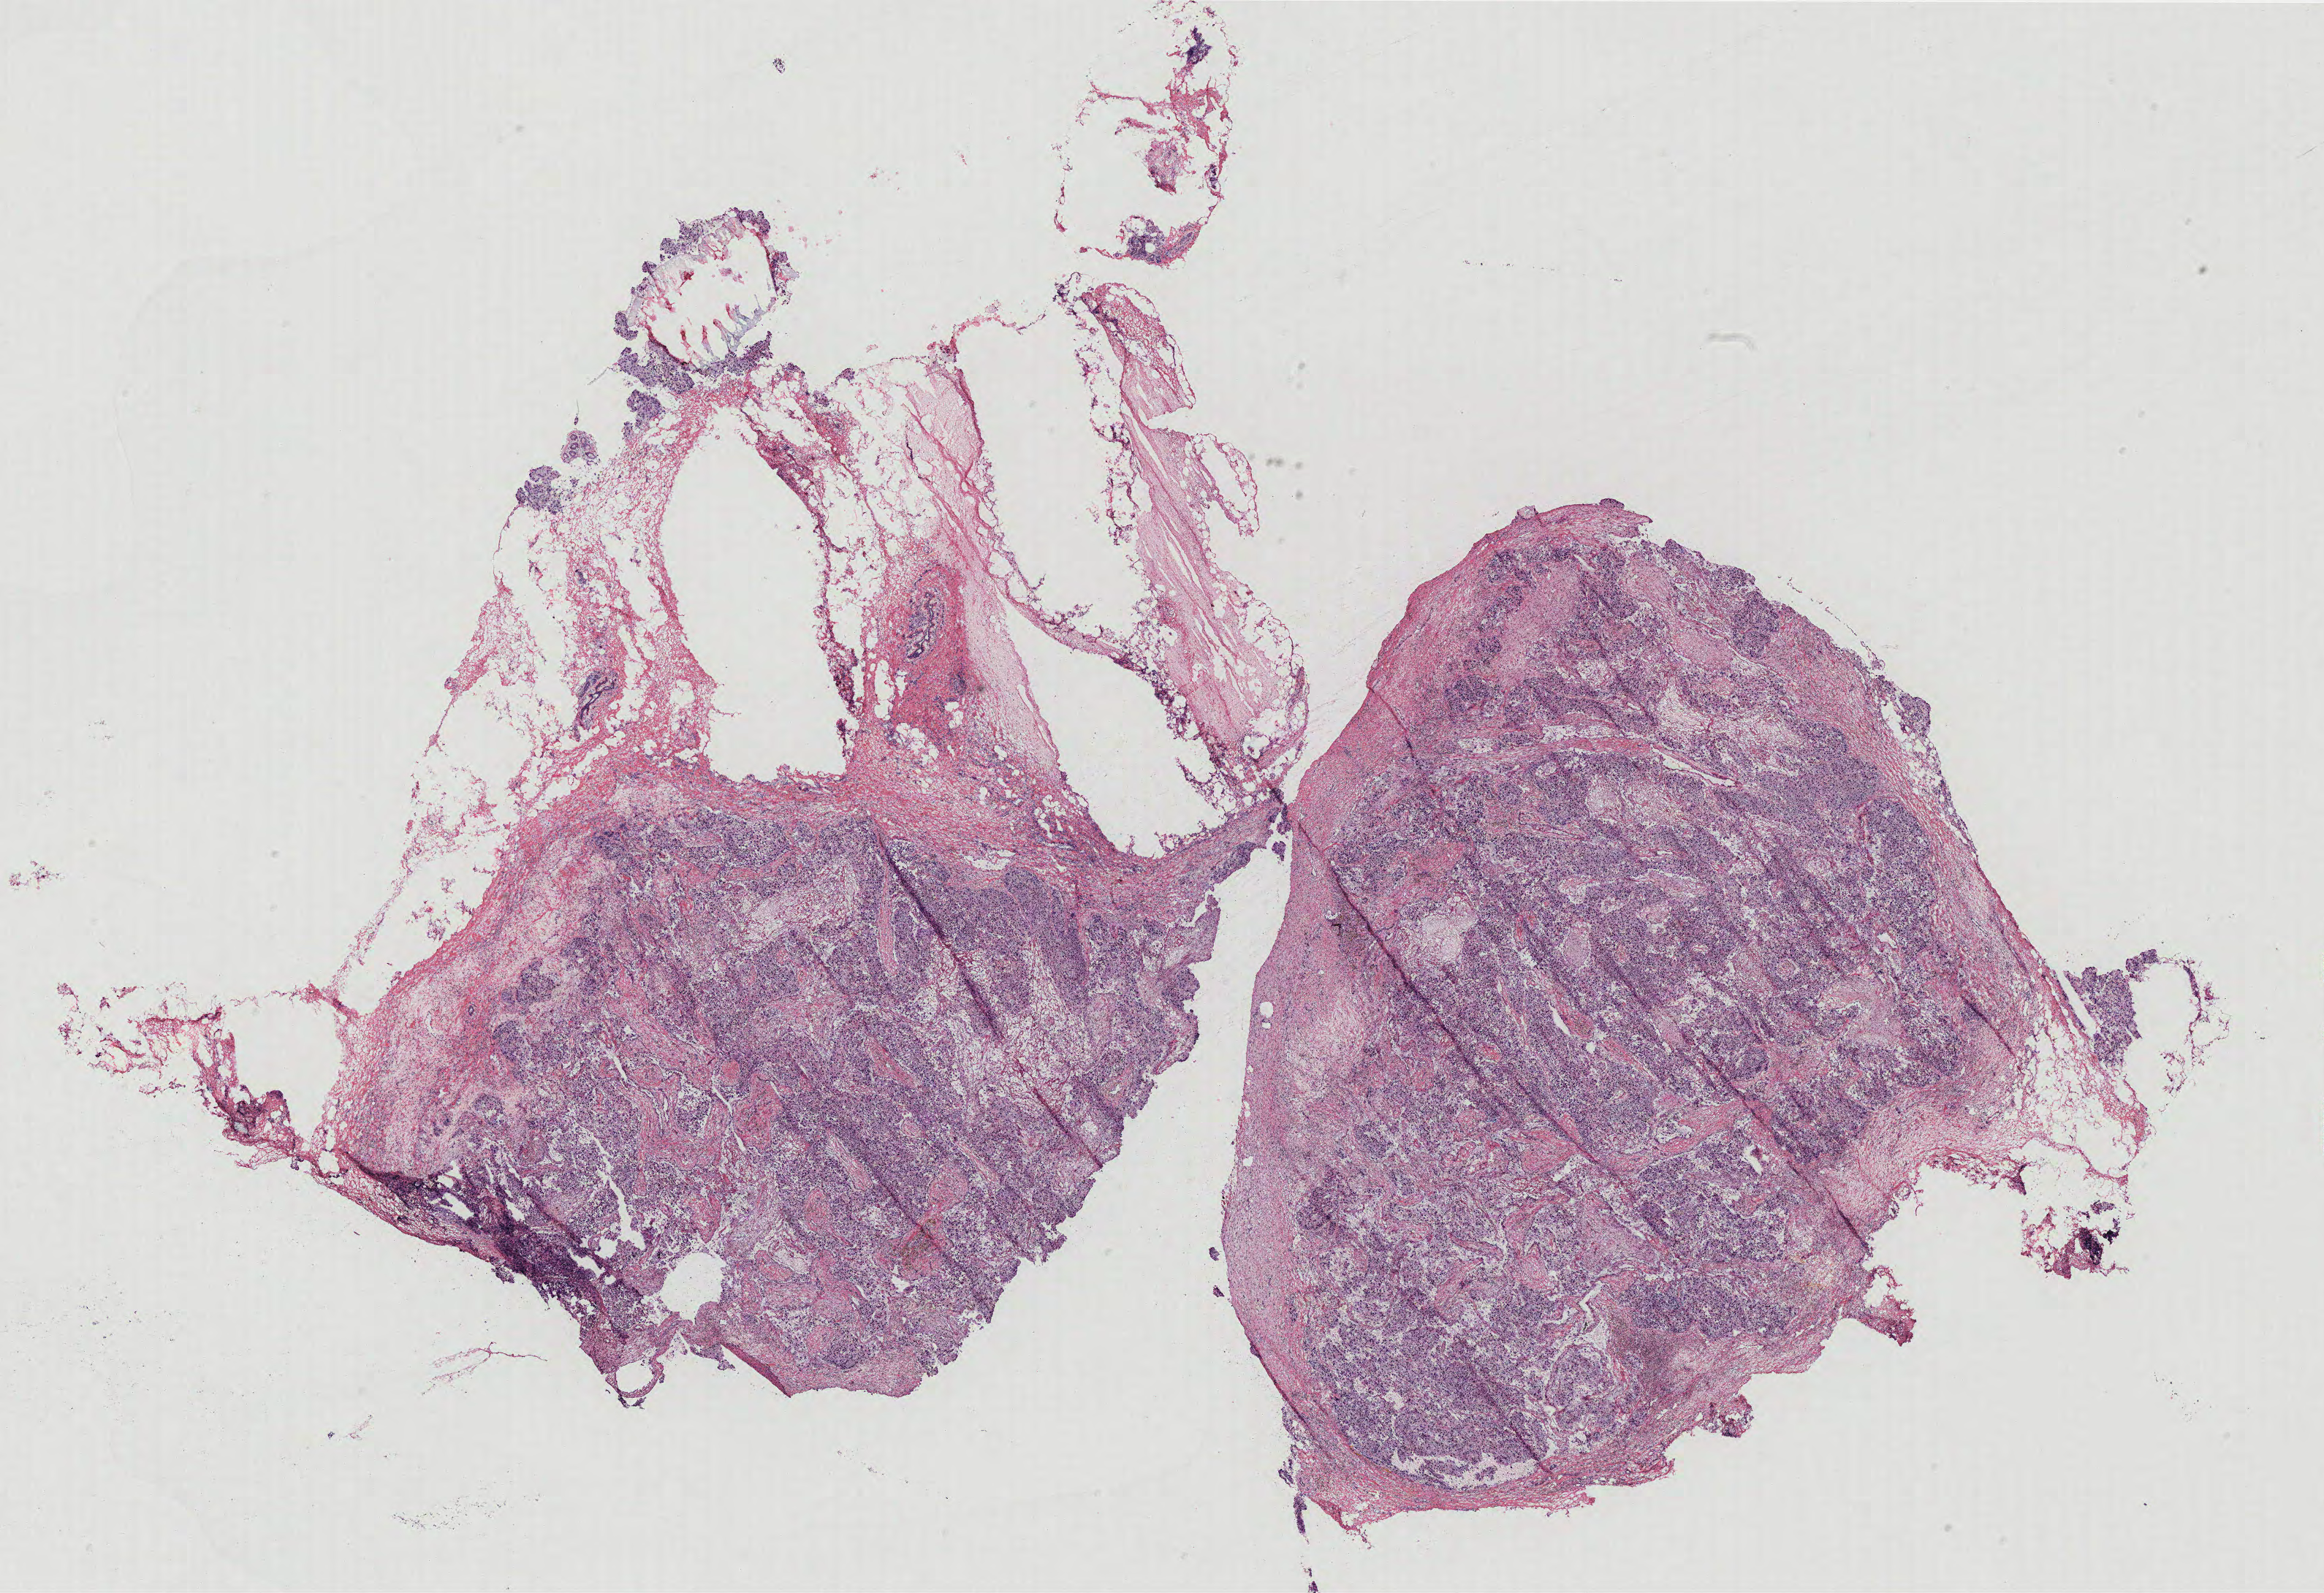
Whole-slide histology image, H&E, whole scanned area (about 25.5 x 17.4 mm, slide scanned at 40x) shown as a low-resolution overview; breast, tissue type not recorded.
- patient diagnosis (cohort enrolment): breast cancer (breast)